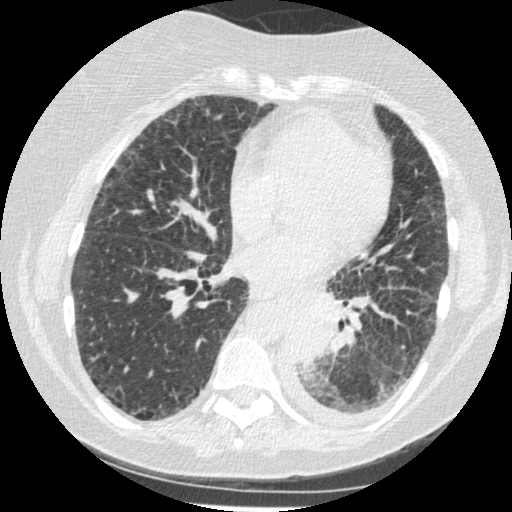
Low-dose screening chest CT, one axial slice; position 96 of 341 along the scan axis; lung window (W 1500 / L -600 HU); 512 × 512 image matrix, field of view 310 × 310 mm.
Structures marked on this image (manually delineated by an expert):
- lesion 1 (tumor, lower lobe of left lung): box from (x=288, y=309) to (x=332, y=365) px